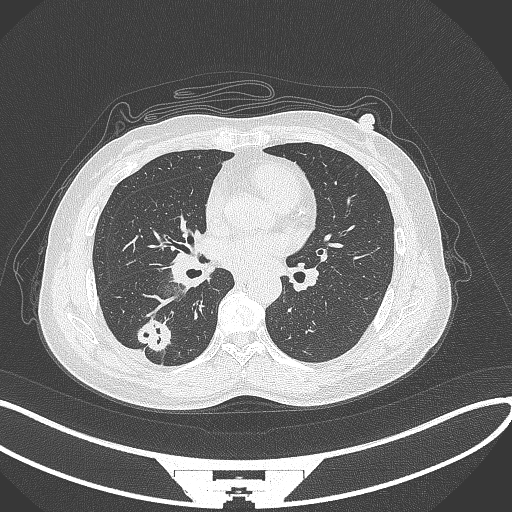
Chest CT, one axial slice. Slice 145 of 352 in the series (ordered by position). 120 kVp. Lung window (W 1500 / L -600 HU). 1 mm slice thickness. 512 × 512 image matrix. Female patient, age 55 years. Case-level facts recorded for this patient, not image findings: clinical TNM (as recorded): T1c N1 M0.
Annotated regions visible in this slice (bounding box drawn by a radiologist):
- lung tumour (recorded histology: adenocarcinoma): bounding box (x1, y1, x2, y2) in pixels: (134, 312, 174, 357)